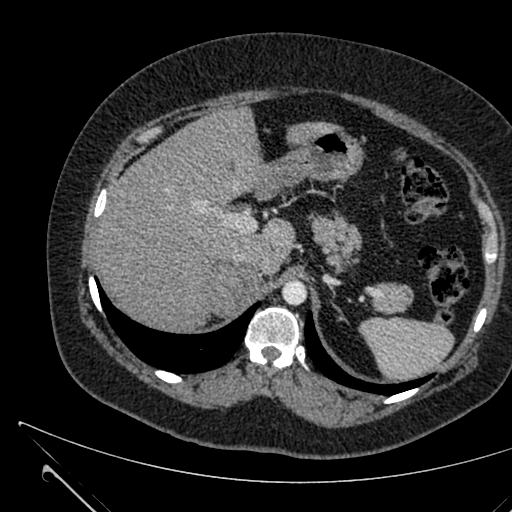
Contrast-enhanced abdominal CT, one axial slice; slice 477 of 731 in the series (ordered by position); 120 kVp; soft-tissue window (W 400 / L 40 HU); 1 mm slice thickness; 512 × 512 image matrix, field of view 376 × 376 mm. Patient: female, 36 years. Case-level facts recorded for this patient, not image findings: diagnosis: adrenocortical carcinoma; tumour side: right adrenal; tumour size at pathology: 10 cm; Ki-67 index: 20 %.
Annotated regions visible in this slice (semi-automatically segmented with operator editing):
- mass: box from (x=207, y=269) to (x=265, y=316) px